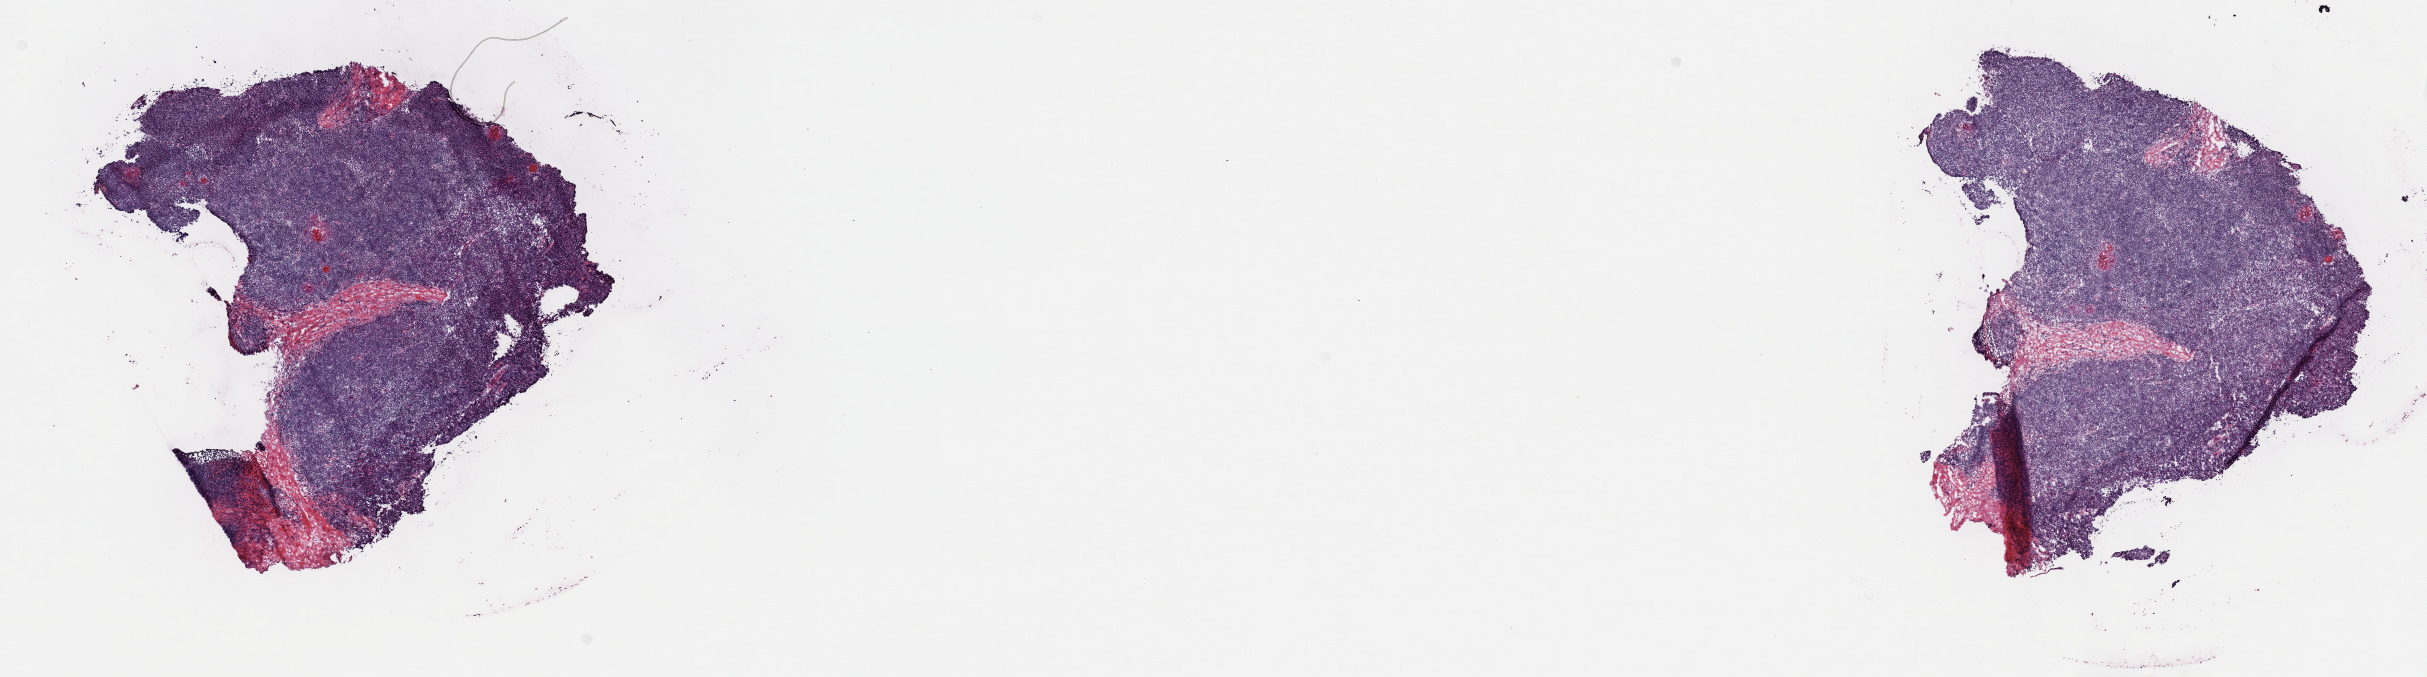
Whole-slide histology image, Hematoxylin and eosin (H&E) stained, low-resolution overview of the scanned area, about 19.6 x 5.5 mm (slide scanned at 40x). Frozen section from the top of the tissue portion. Primary tumour sample from the thymus. Male patient; age at initial diagnosis 63 years. Pathologist review of this section (percent, as recorded): tumour cells 80%, tumour nuclei 80%, normal cells 0%, stromal cells 20%, necrosis 0%. Inflammatory infiltration, as recorded: lymphocyte infiltration 3%, monocyte infiltration 1%, neutrophil infiltration 1%.
Pathologic diagnosis: Thymoma, type B3, malignant.